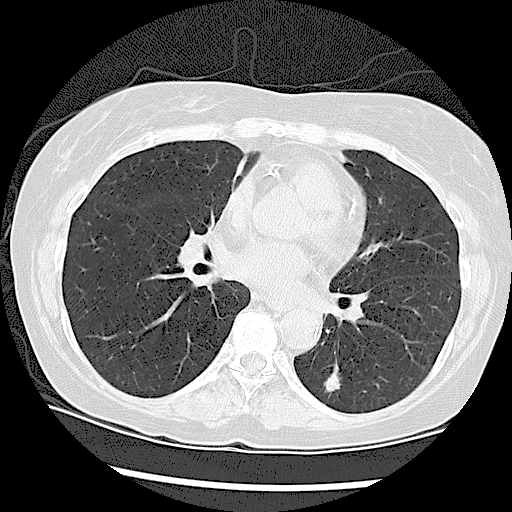
Chest CT (low-dose screening protocol), one axial image, second screening round (one year after baseline), lung window (W 1500 / L -600 HU), 120 kVp. Female, age 61 years at enrolment.
Expert reader's lesion annotation, bounding box <305,360,359,406> (left, top, right, bottom; pixels). The screening reader recorded 2 non-calcified nodules or masses ≥4 mm on this exam (left lower lobe, right lower lobe); which of them this box marks is not recorded. Official screen result: positive, other. Lung cancer was diagnosed 178 days after this screen: adenocarcinoma, NOS, left lower lobe, moderately differentiated (G2), stage IA (AJCC 6th edition), 18 mm at pathology.